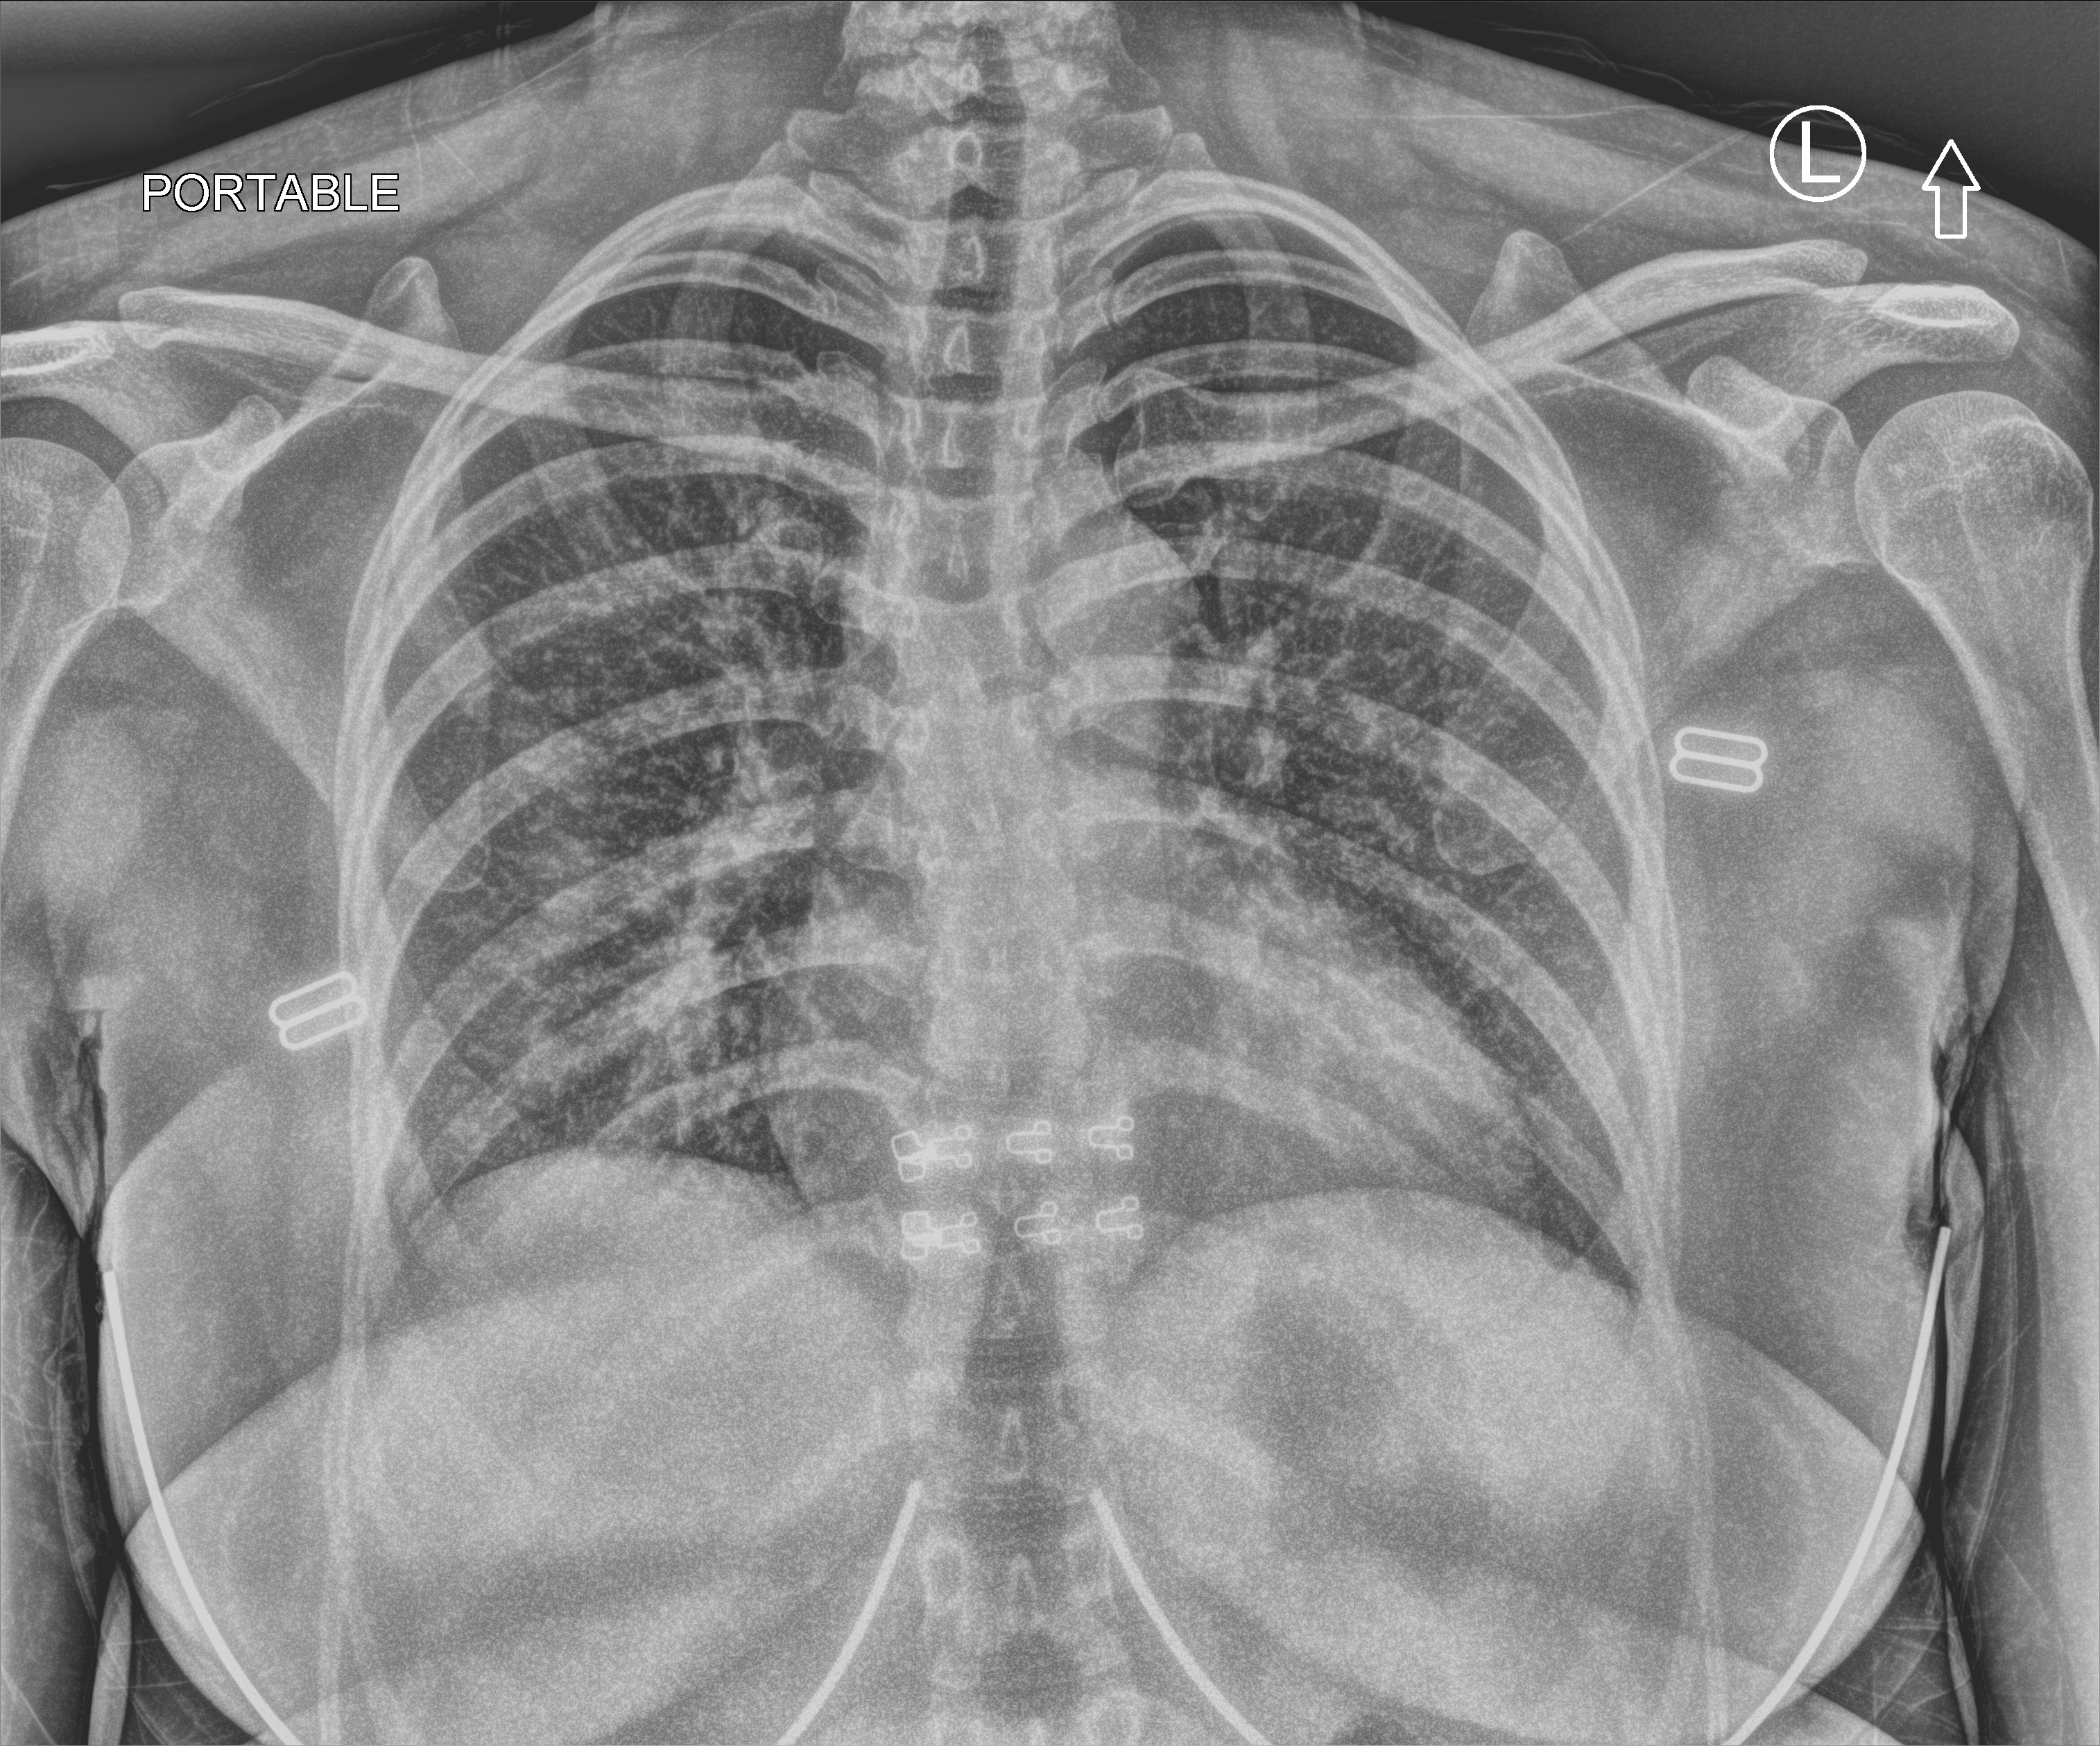
Bedside chest radiograph (computed radiography); anteroposterior (AP) projection. Female patient hospitalised with COVID-19, age 18–59 years.
Hospital-stay facts (about this admission, not read from this image; timing relative to this image not recorded): length of hospital stay: 2 days.